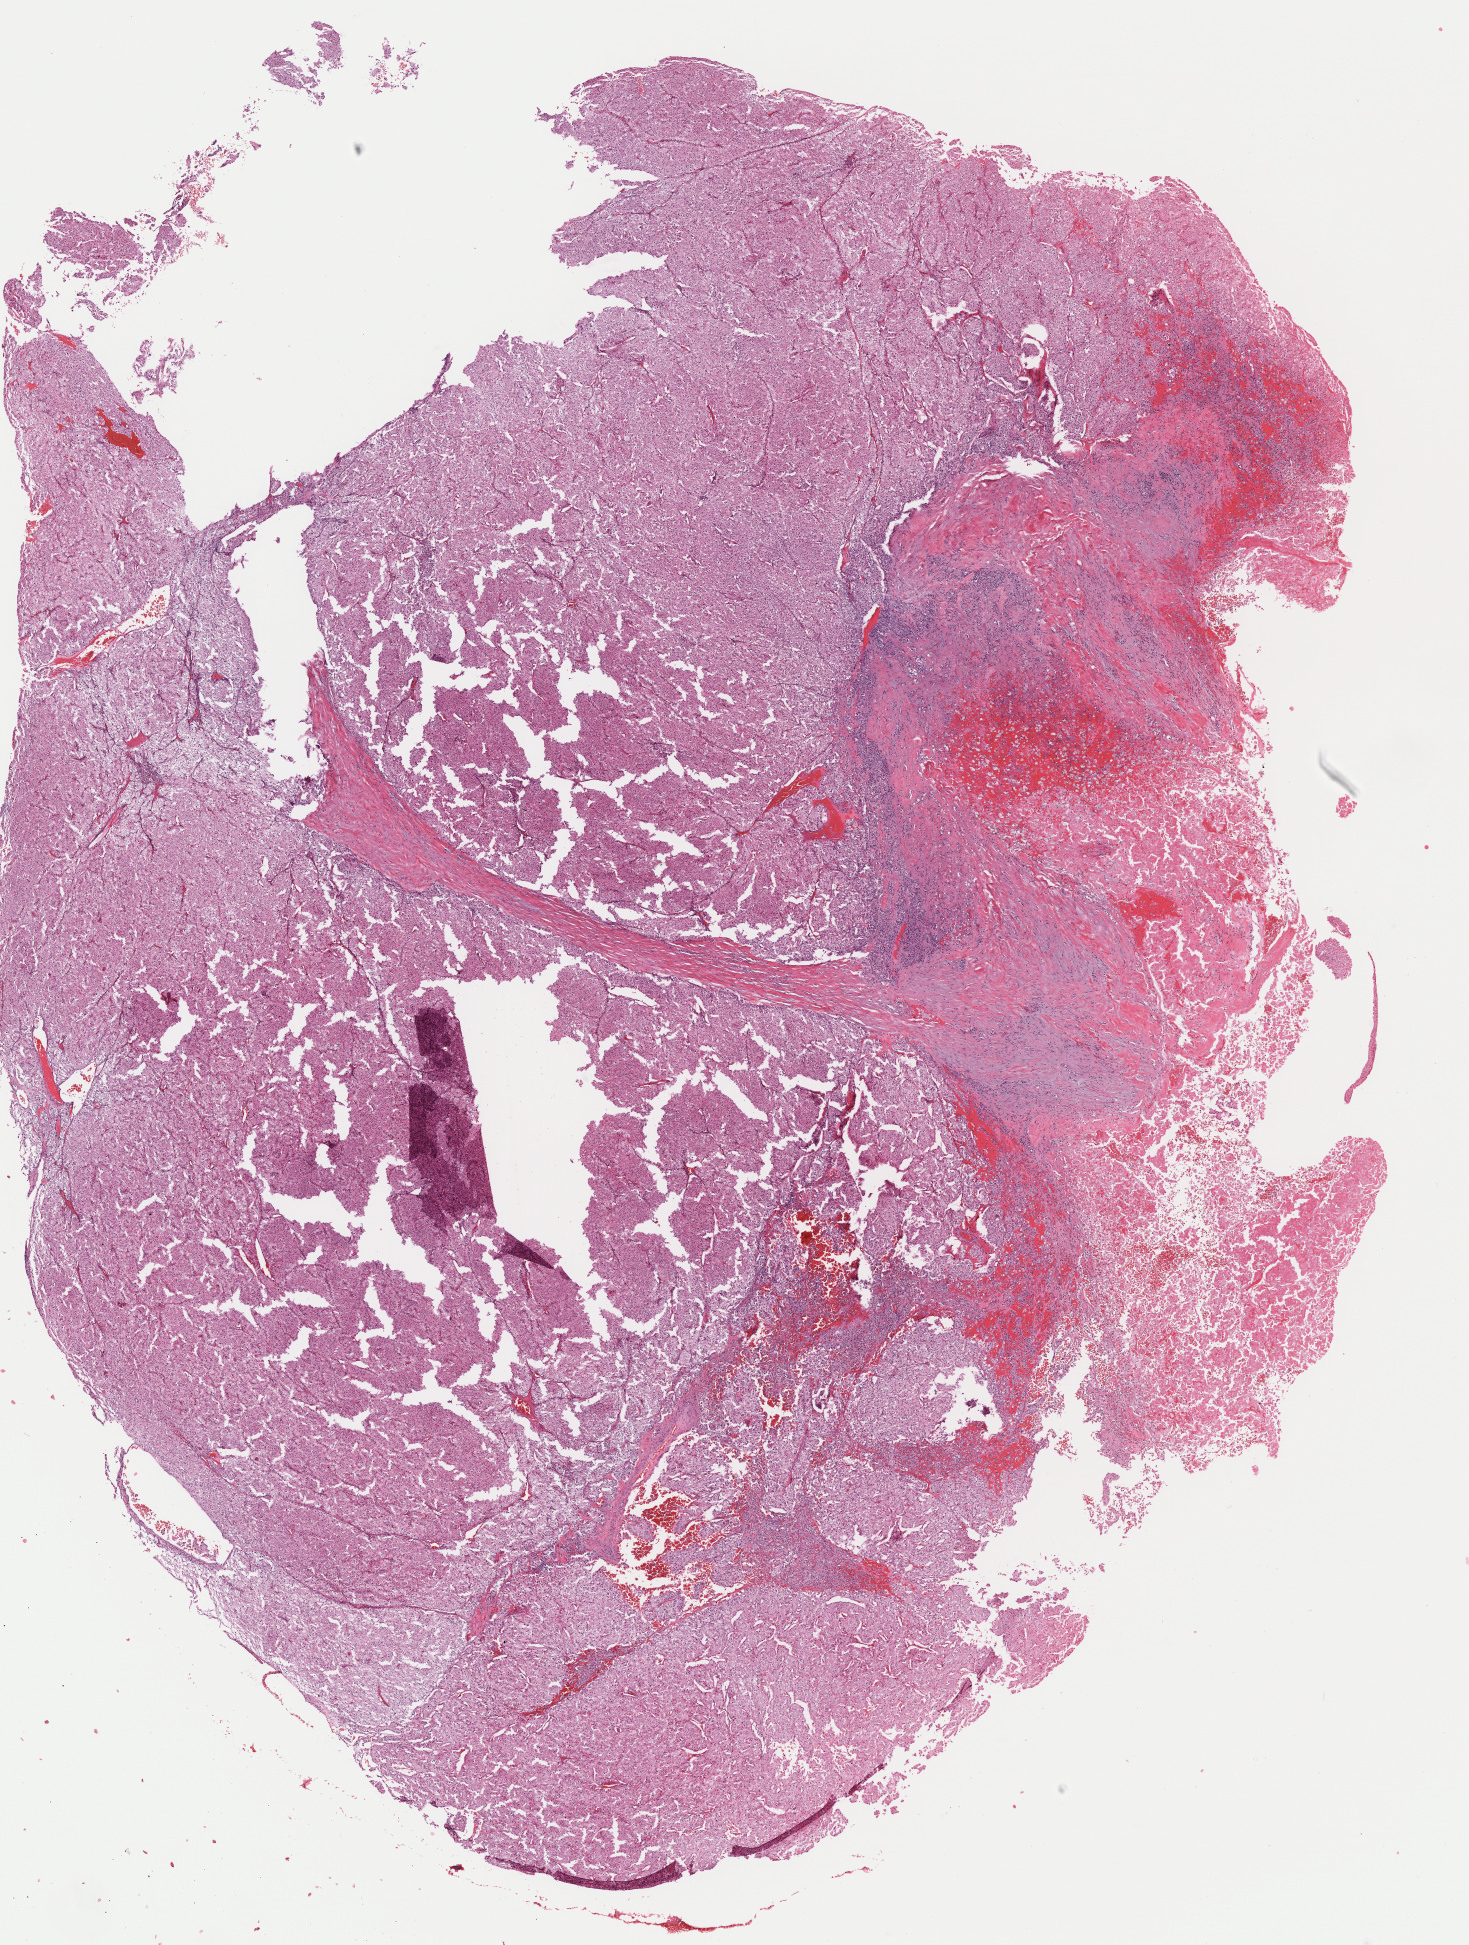
Digitized H&E tissue section (whole slide) — whole scanned area (about 11.8 x 15.7 mm, acquisition: 40x scan) shown as a low-resolution overview, formalin-fixed paraffin-embedded (FFPE) diagnostic section, primary tumour sample from the kidney. Male, age 50 years at initial diagnosis.
TNM: T3a NX M1. AJCC pathologic stage: IV (6th edition). Diagnosis: Renal cell carcinoma, chromophobe type.